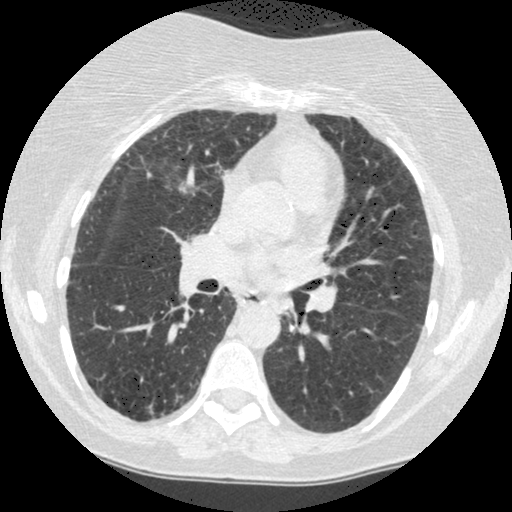
Low-dose screening chest CT, axial slice, baseline screening round, lung window (W 1500 / L -600 HU), standard (soft-tissue) reconstruction kernel (STANDARD), 120 kVp, slice 207 of 442 in the series. Female, age 60 years at enrolment. Former smoker at enrolment.
• Expert reader's lesion annotation, bounding box <266,291,308,332> (left, top, right, bottom; pixels).
• The screening reader recorded 2 non-calcified nodules or masses ≥4 mm on this exam (right lower lobe, left lower lobe); which of them this box marks is not recorded.
• Official screen result: positive, change unspecified: nodule(s) >= 4 mm or enlarging nodule(s), mass(es), or other non-specific abnormalities suspicious for lung cancer.
• Later outcome: lung cancer diagnosed 794 days after this screen (after the third annual screen) — small cell carcinoma, NOS, left lower lobe, undifferentiated (G4), stage IV (AJCC 6th edition), 69 mm at pathology.